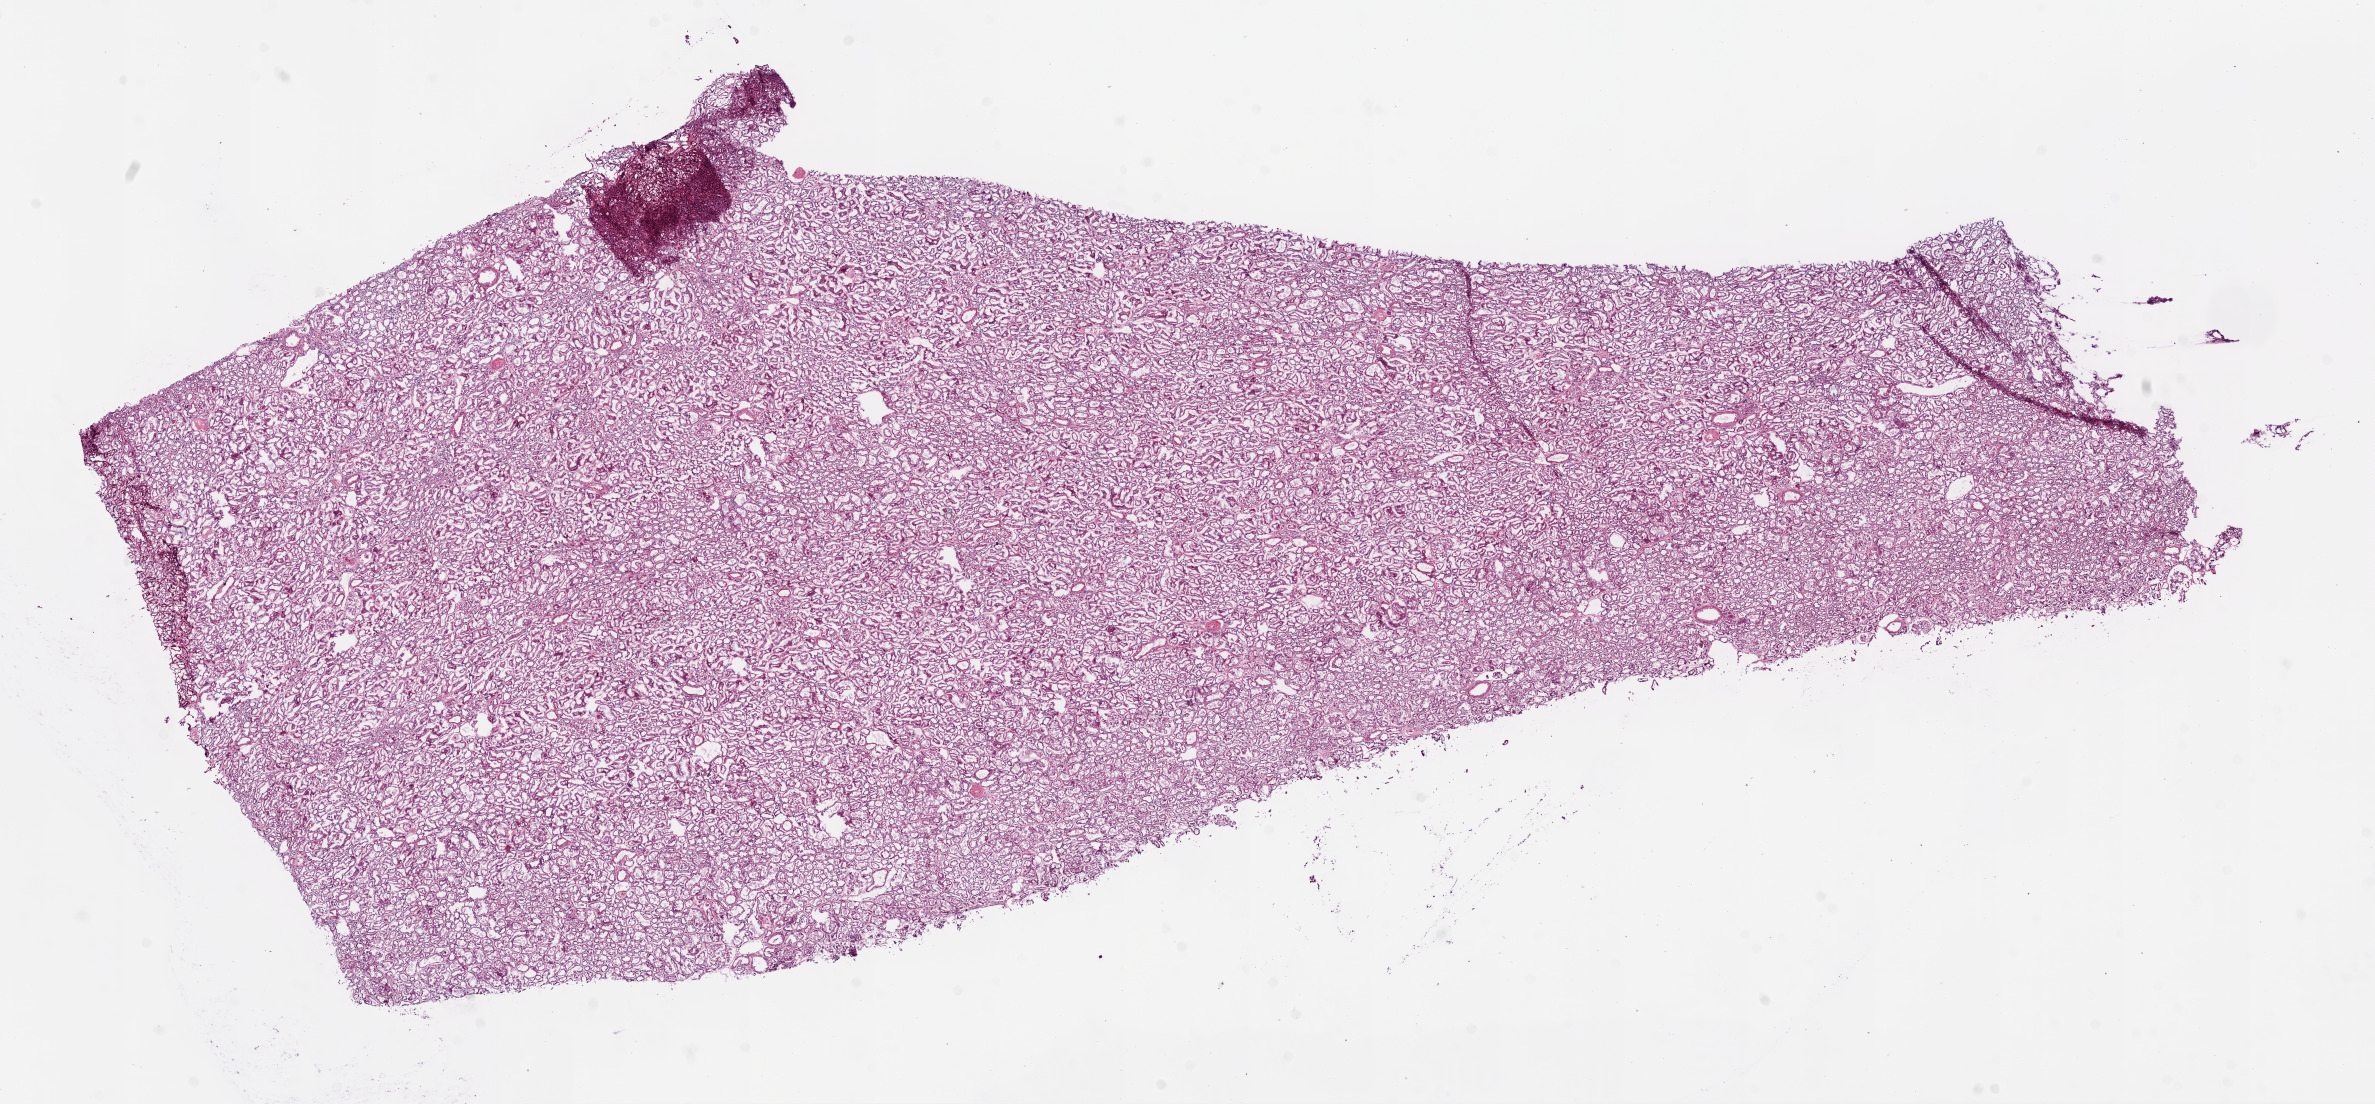
Hematoxylin and eosin (H&E) stained whole-slide image, whole scanned area (about 19.1 x 8.9 mm, acquisition: 20x scan) shown as a low-resolution overview; frozen section from the bottom of the tissue portion; kidney, solid tissue normal (non-tumour tissue) sample. Patient: female, age at initial diagnosis 73 years.
* this section: solid tissue normal (non-tumour) sample from the same patient
* patient diagnosis: Clear cell adenocarcinoma, NOS